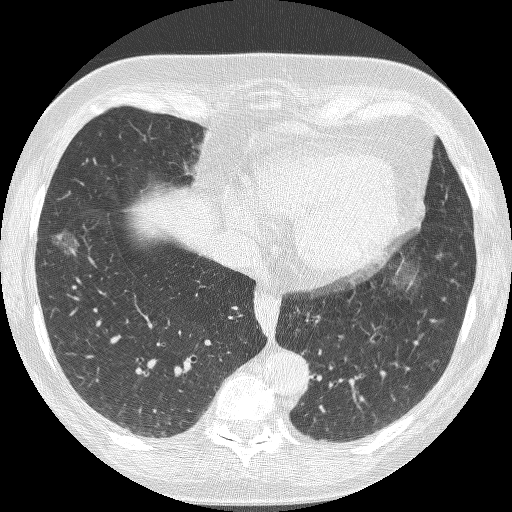
Chest CT (low-dose screening protocol), one axial image, baseline screening round, lung window (W 1500 / L -600 HU), slice 72 of 221 in the series. Female, age 68 years at enrolment. Current smoker at enrolment.
- Expert-annotated lung lesion, bounding box <33,225,85,278> (left, top, right, bottom; pixels).
- Reader record for this screening exam (exam-level; its link to the box is not recorded): non-calcified nodule or mass ≥4 mm, right lower lobe, 16 × 12 mm, poorly defined margins, ground glass attenuation.
- Lung cancer was diagnosed 406 days after this screen (after the second annual screen): bronchiolo-alveolar adenocarcinoma, NOS, right lower lobe, well differentiated (G1), stage IA (AJCC 6th edition), 13 mm at pathology.